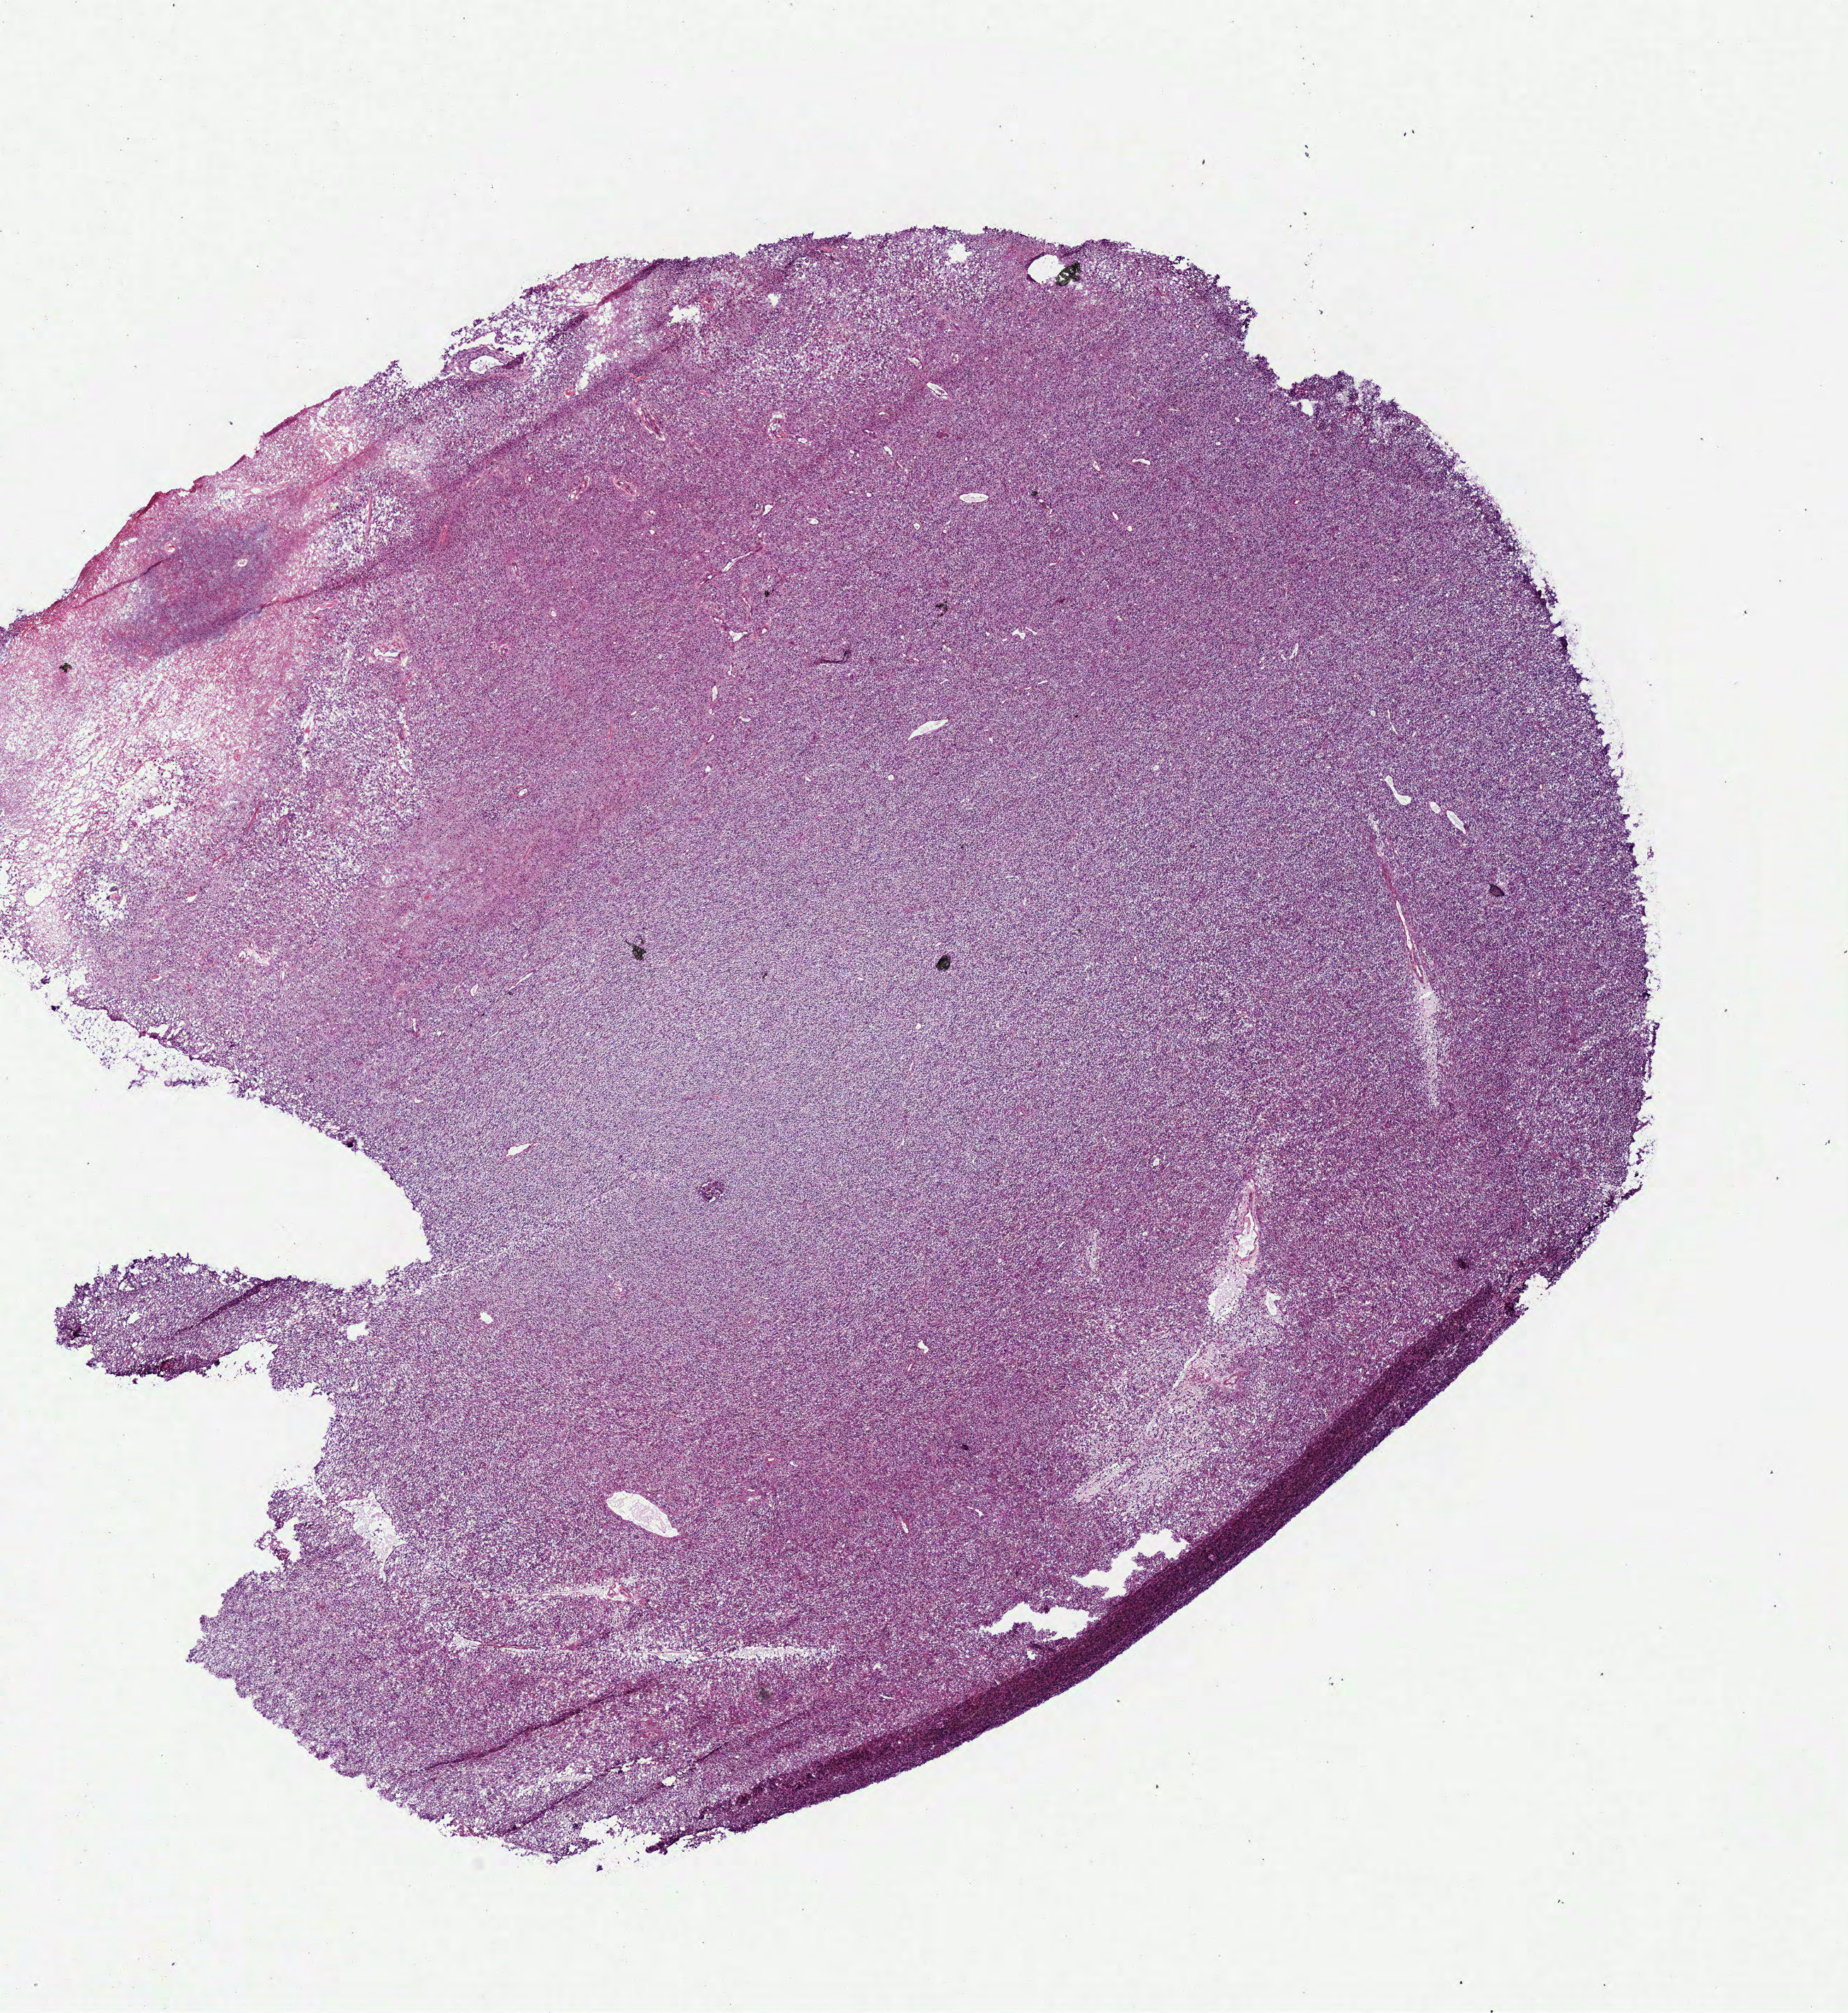
H&E whole-slide image, low-resolution overview of the scanned area, about 10.3 x 11.2 mm; frozen section from the bottom of the tissue portion; brain, primary tumour sample. Patient: female, age at initial diagnosis 59 years. Histologic grade: G3 (poorly differentiated). Slide review estimates, as recorded: tumour cells 95%, tumour nuclei 85%, normal cells 0%, stromal cells 0%, necrosis 5%.
Pathologic diagnosis: Mixed glioma (cerebrum).